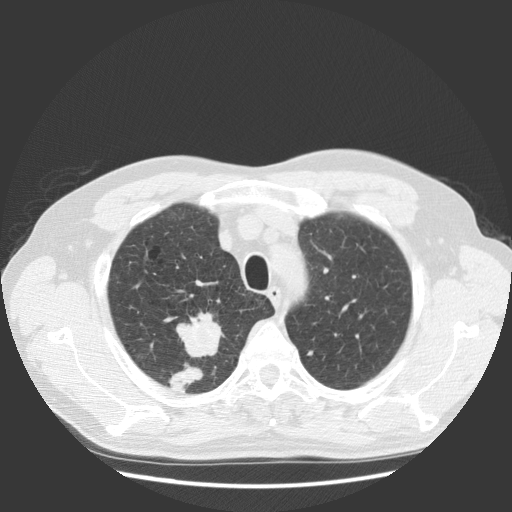
Chest CT (low-dose screening protocol), one axial image; first (baseline) screen; lung window (W 1500 / L -600 HU); 2.5 mm slice thickness; standard (soft-tissue) reconstruction kernel (STANDARD); 140 kVp; slice 103 of 131 in the series; 512 × 512 image matrix. Male participant, aged 63 years at enrolment. Current smoker at enrolment.
Expert reader's lesion annotation, bounding box (x1, y1, x2, y2) in pixels: (162, 311, 234, 380). The screening reader recorded 2 non-calcified nodules or masses ≥4 mm on this exam (right upper lobe, right upper lobe); which of them this box marks is not recorded. Participant outcome: lung cancer diagnosed 30 days after this screen — squamous cell carcinoma, NOS, right upper lobe, stage IIIB (AJCC 6th edition), 35 mm at pathology.